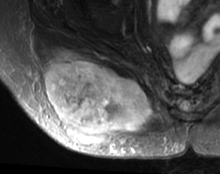
MRI of an extremity soft-tissue mass, one axial slice; position 24 of 63 along the scan axis; T2-weighted fat-saturated; MR volume resampled by the dataset authors to the PET/CT grid (not the native acquisition matrix); 220 × 174 image matrix, field of view 215 × 170 mm. Female patient. Case-level facts recorded for this patient, not image findings: histological type: spindle cell suggestive of myxofibrosarcoma; grade: intermediate; site of the primary tumour: right buttock.
Structures marked on this image (expert contour drawn on MRI and transferred to this co-registered scan by the dataset authors):
- gross tumour volume (mass): box from (x=42, y=50) to (x=153, y=149) px